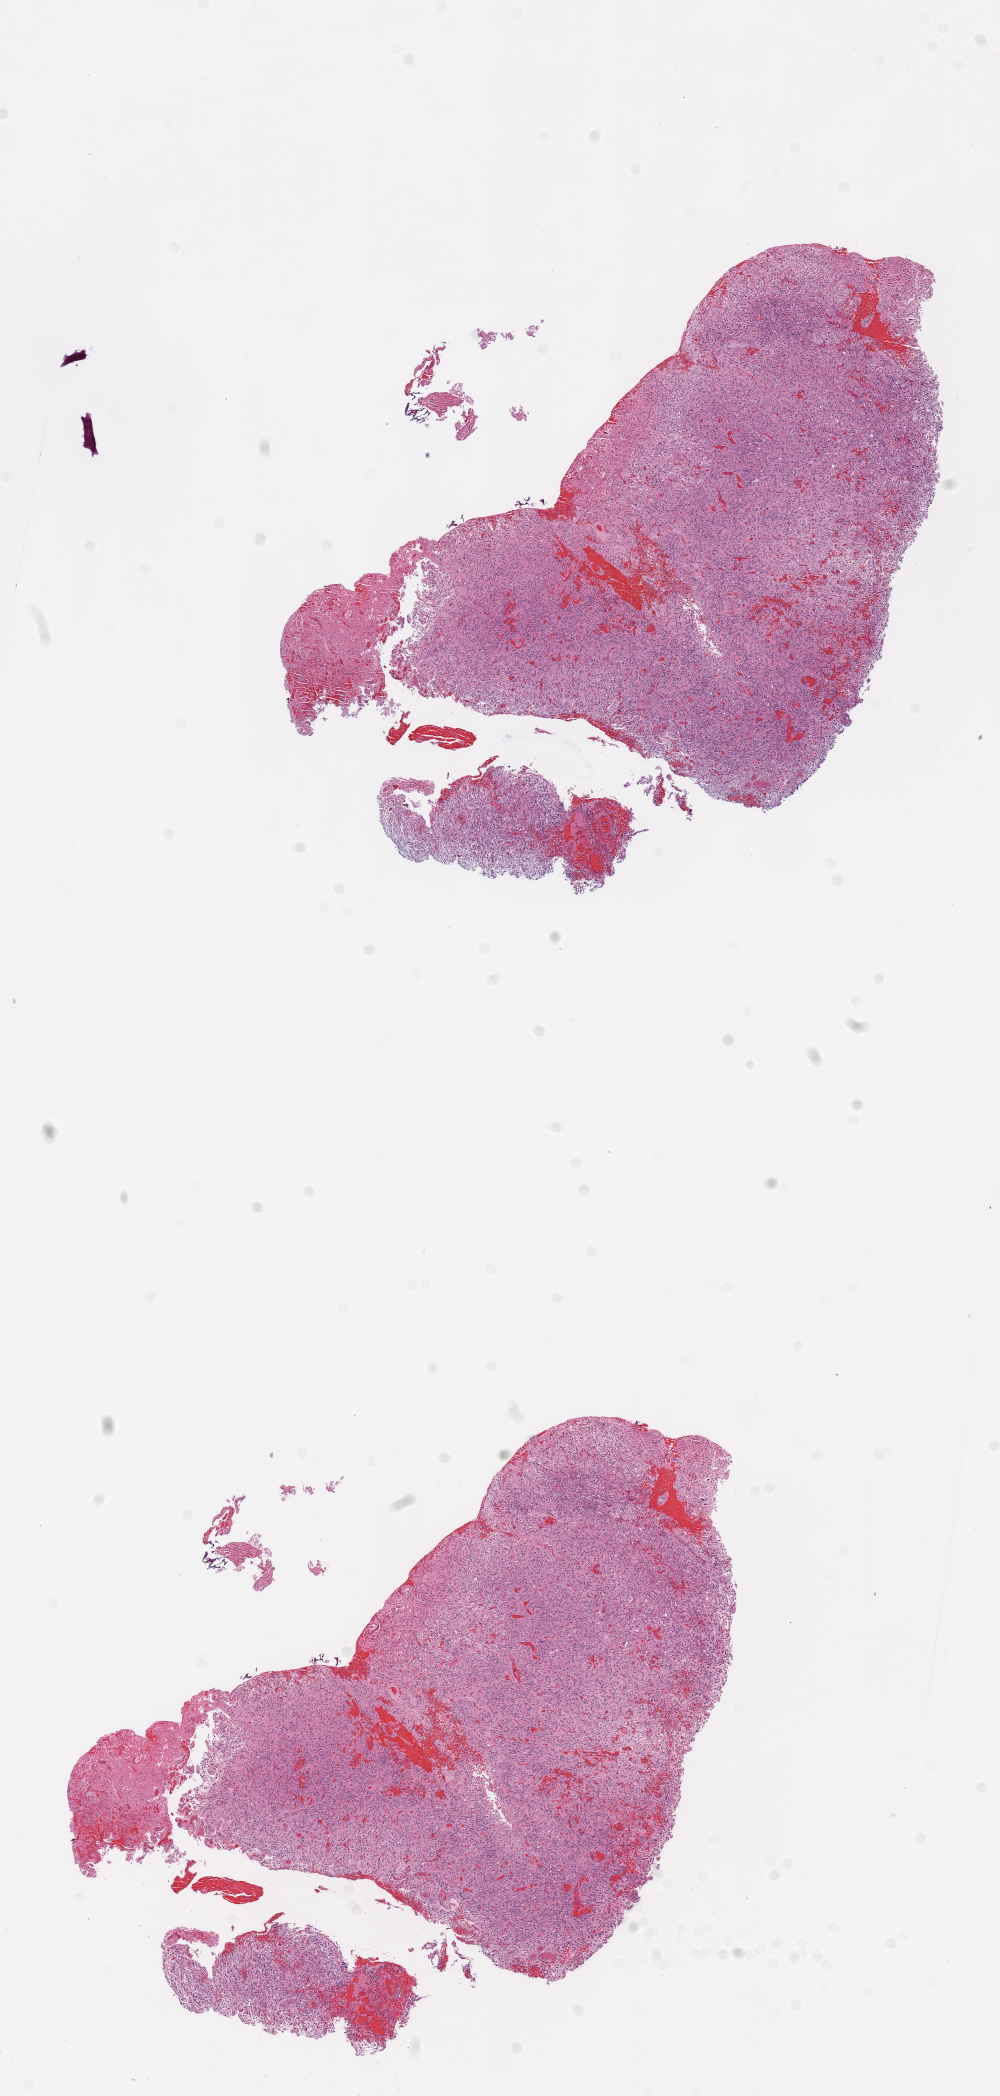
H&E whole-slide image, low-resolution overview of the scanned area, about 8.0 x 16.8 mm (from a 20x scan), formalin-fixed paraffin-embedded (FFPE) diagnostic section, brain, primary tumour sample. Patient: male, age at initial diagnosis 78 years.
Pathologic diagnosis: Glioblastoma.